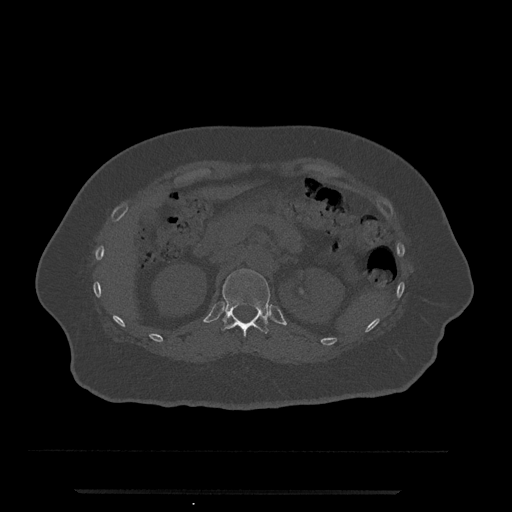
CT including the spine, one axial slice; slice 168 of 797 in the series (ordered by position); 120 kVp; bone window (W 1800 / L 400 HU); 512 × 512 image matrix, field of view 440 × 440 mm. Female patient, age 51 years. From the clinical record (not read from this slice): primary cancer: neuro; vertebrae with lytic lesions (as recorded): T8.
Annotated regions visible in this slice (semi-automatically segmented with operator editing):
- T12 vertebra: bounding box (x1, y1, x2, y2) in pixels: (222, 269, 270, 336)